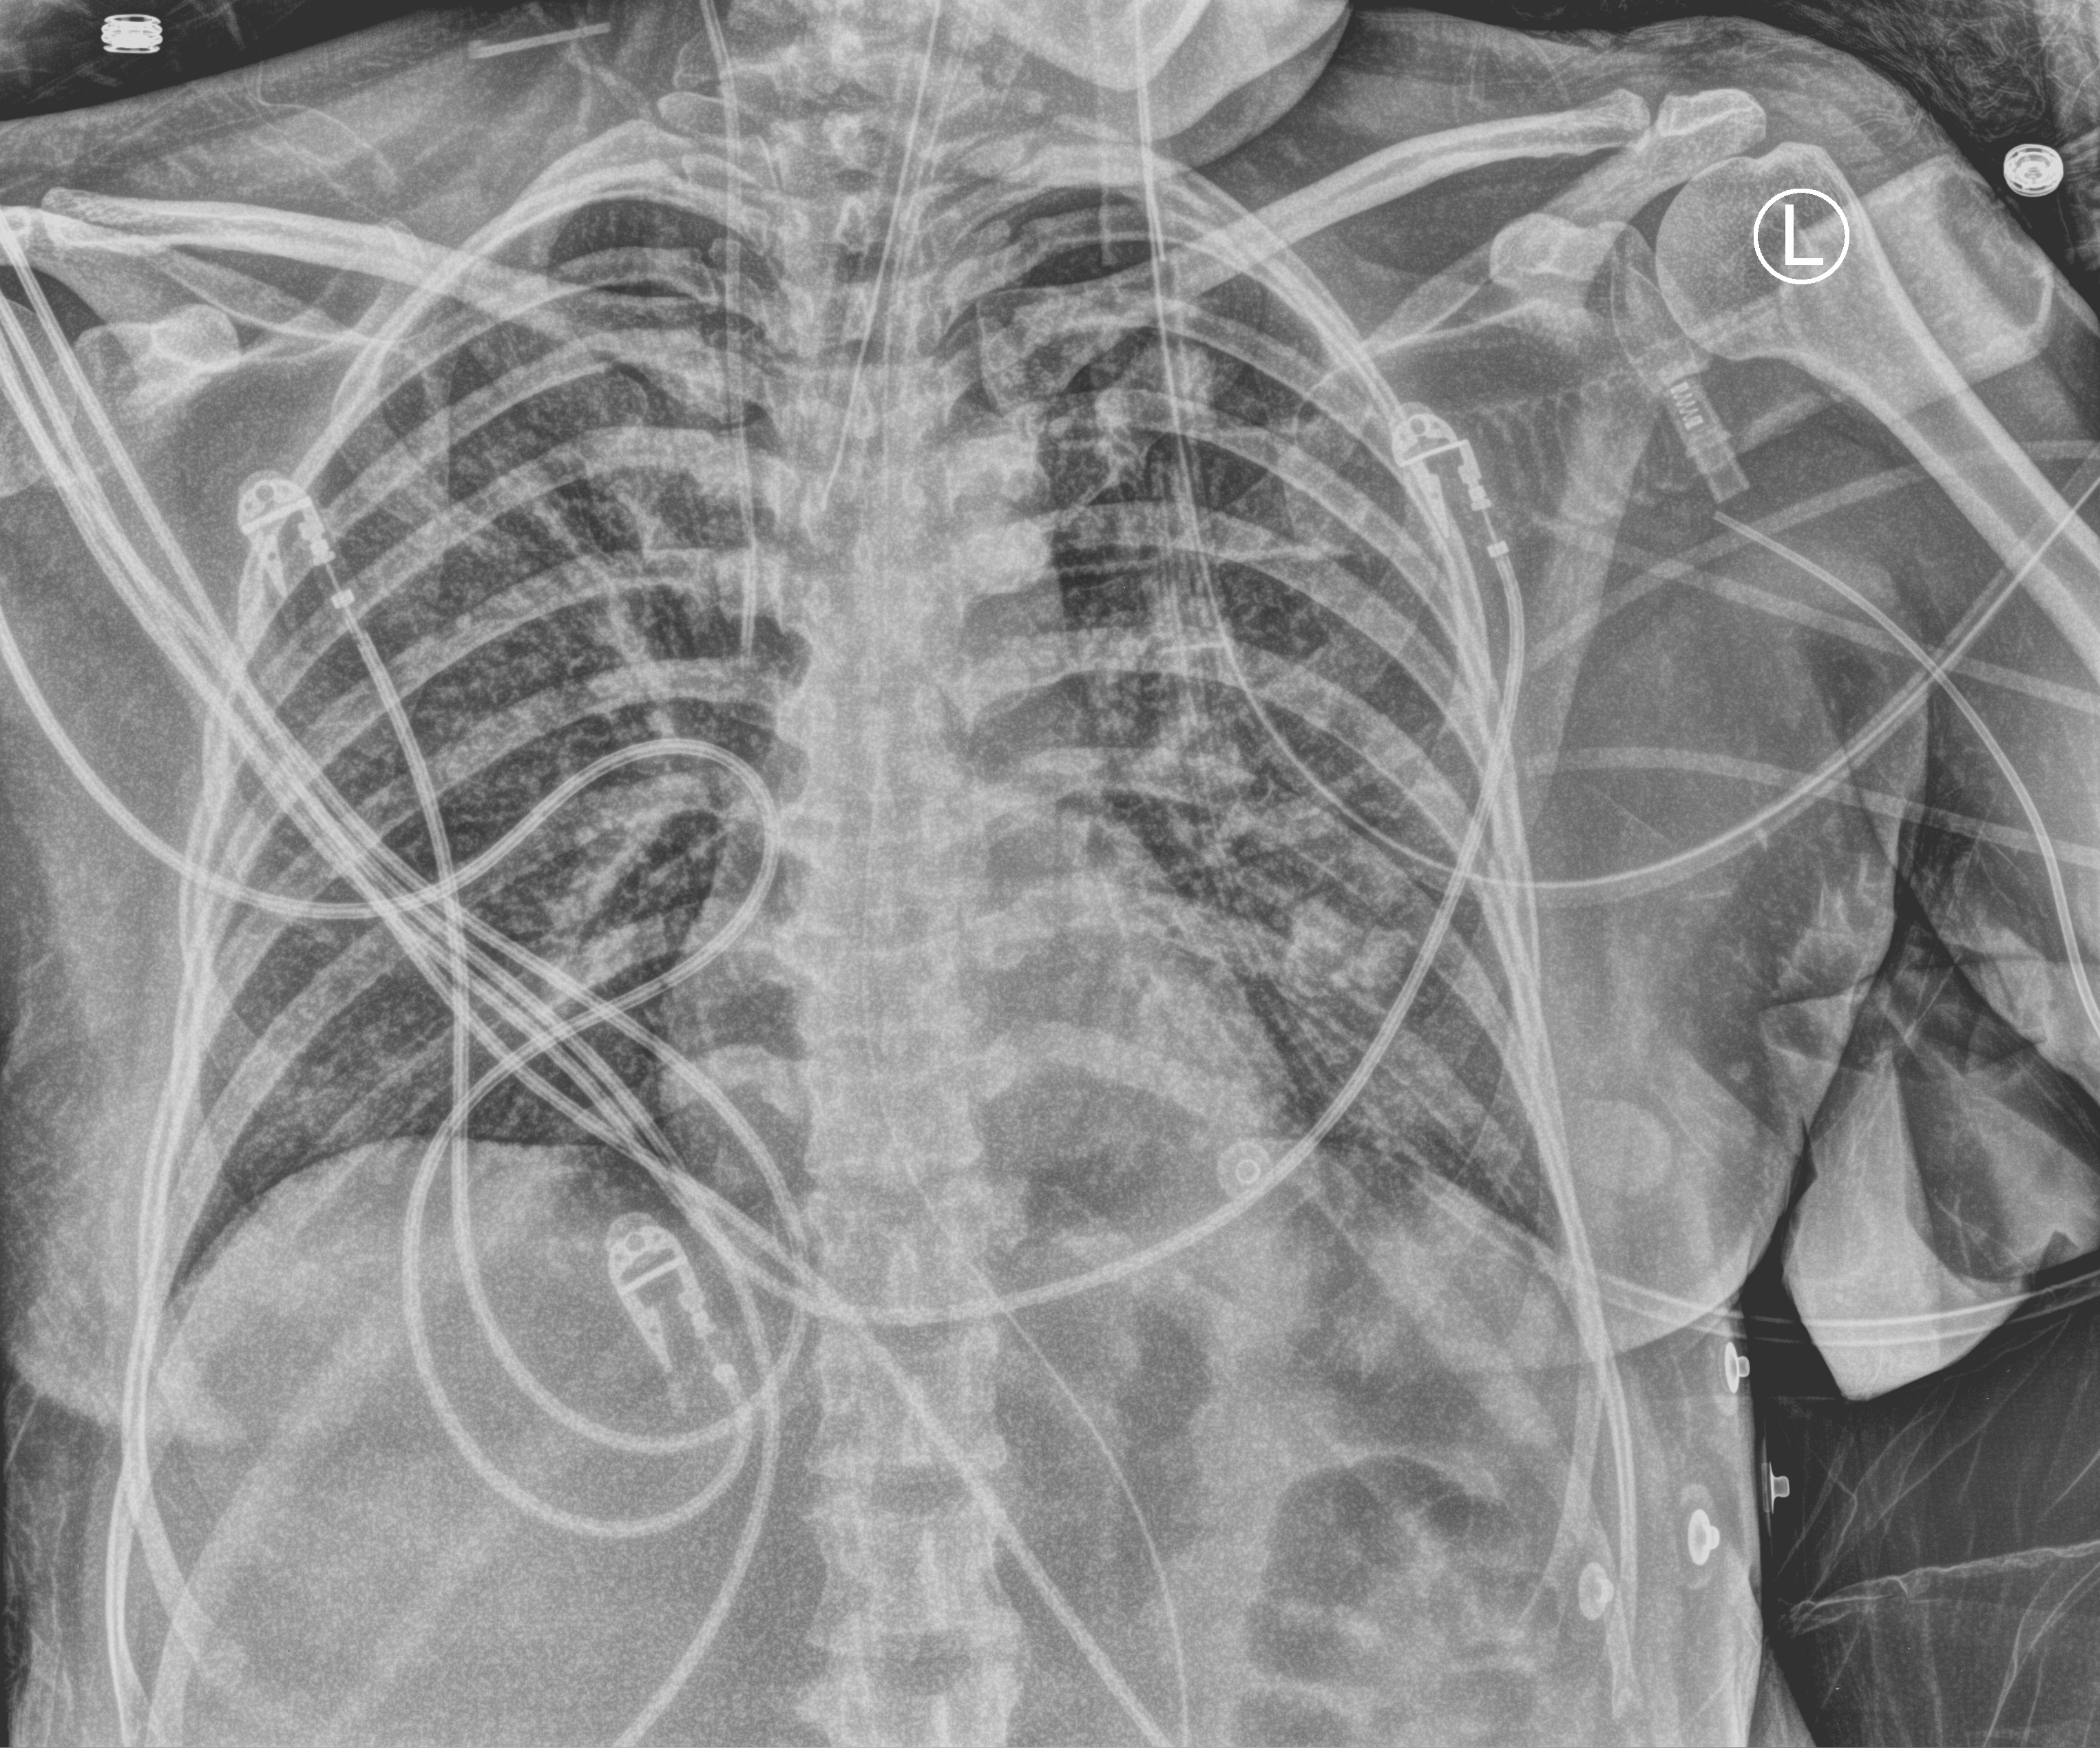
Portable chest radiograph. Patient hospitalised with COVID-19; female, aged 18–59 years.
Hospital-stay facts (about this admission, not read from this image; timing relative to this image not recorded):
- diabetes (admission record): no
- admitted to intensive care during this hospital stay: yes